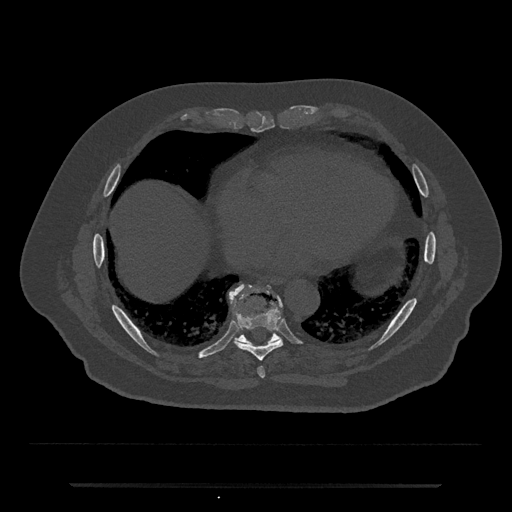
CT including the spine, one axial slice; slice 793 of 797 in the series (ordered by position); reconstruction kernel Br40s/3; 120 kVp; bone window (W 1800 / L 400 HU); 0.5 mm slice thickness; 512 × 512 image matrix, field of view 434 × 434 mm. Patient: male, 80 years. From the clinical record (not read from this slice): primary cancer: prostate.
Annotated regions visible in this slice (semi-automatically segmented with operator editing):
- T8 vertebra: bounding box <234,307,283,361> (left, top, right, bottom; pixels)
- T9 vertebra: <230,284,281,347>